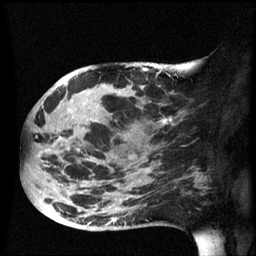
Breast MRI (dynamic contrast-enhanced), one sagittal slice; position 26 of 60 along the scan axis; dynamic contrast-enhanced series, image 2 of 3 at this slice position (ordered by acquisition); 1.5 T; TE 4.2 ms, TR 8.4 ms; 2.5 mm slice thickness; 256 × 256 image matrix, field of view 220 × 220 mm. Female patient, age 49 years.
Annotated regions visible in this slice (semi-automatic segmentation, software-assisted and operator-edited):
- analysis volume of interest (the breast-tissue region the enhancement analysis was run in; not a lesion): bounding box [x1, y1, x2, y2] px = [24, 72, 185, 231]
- tumour enhancement mask (voxels above the 70 % enhancement threshold inside the analysis volume of interest): [56, 84, 173, 223]